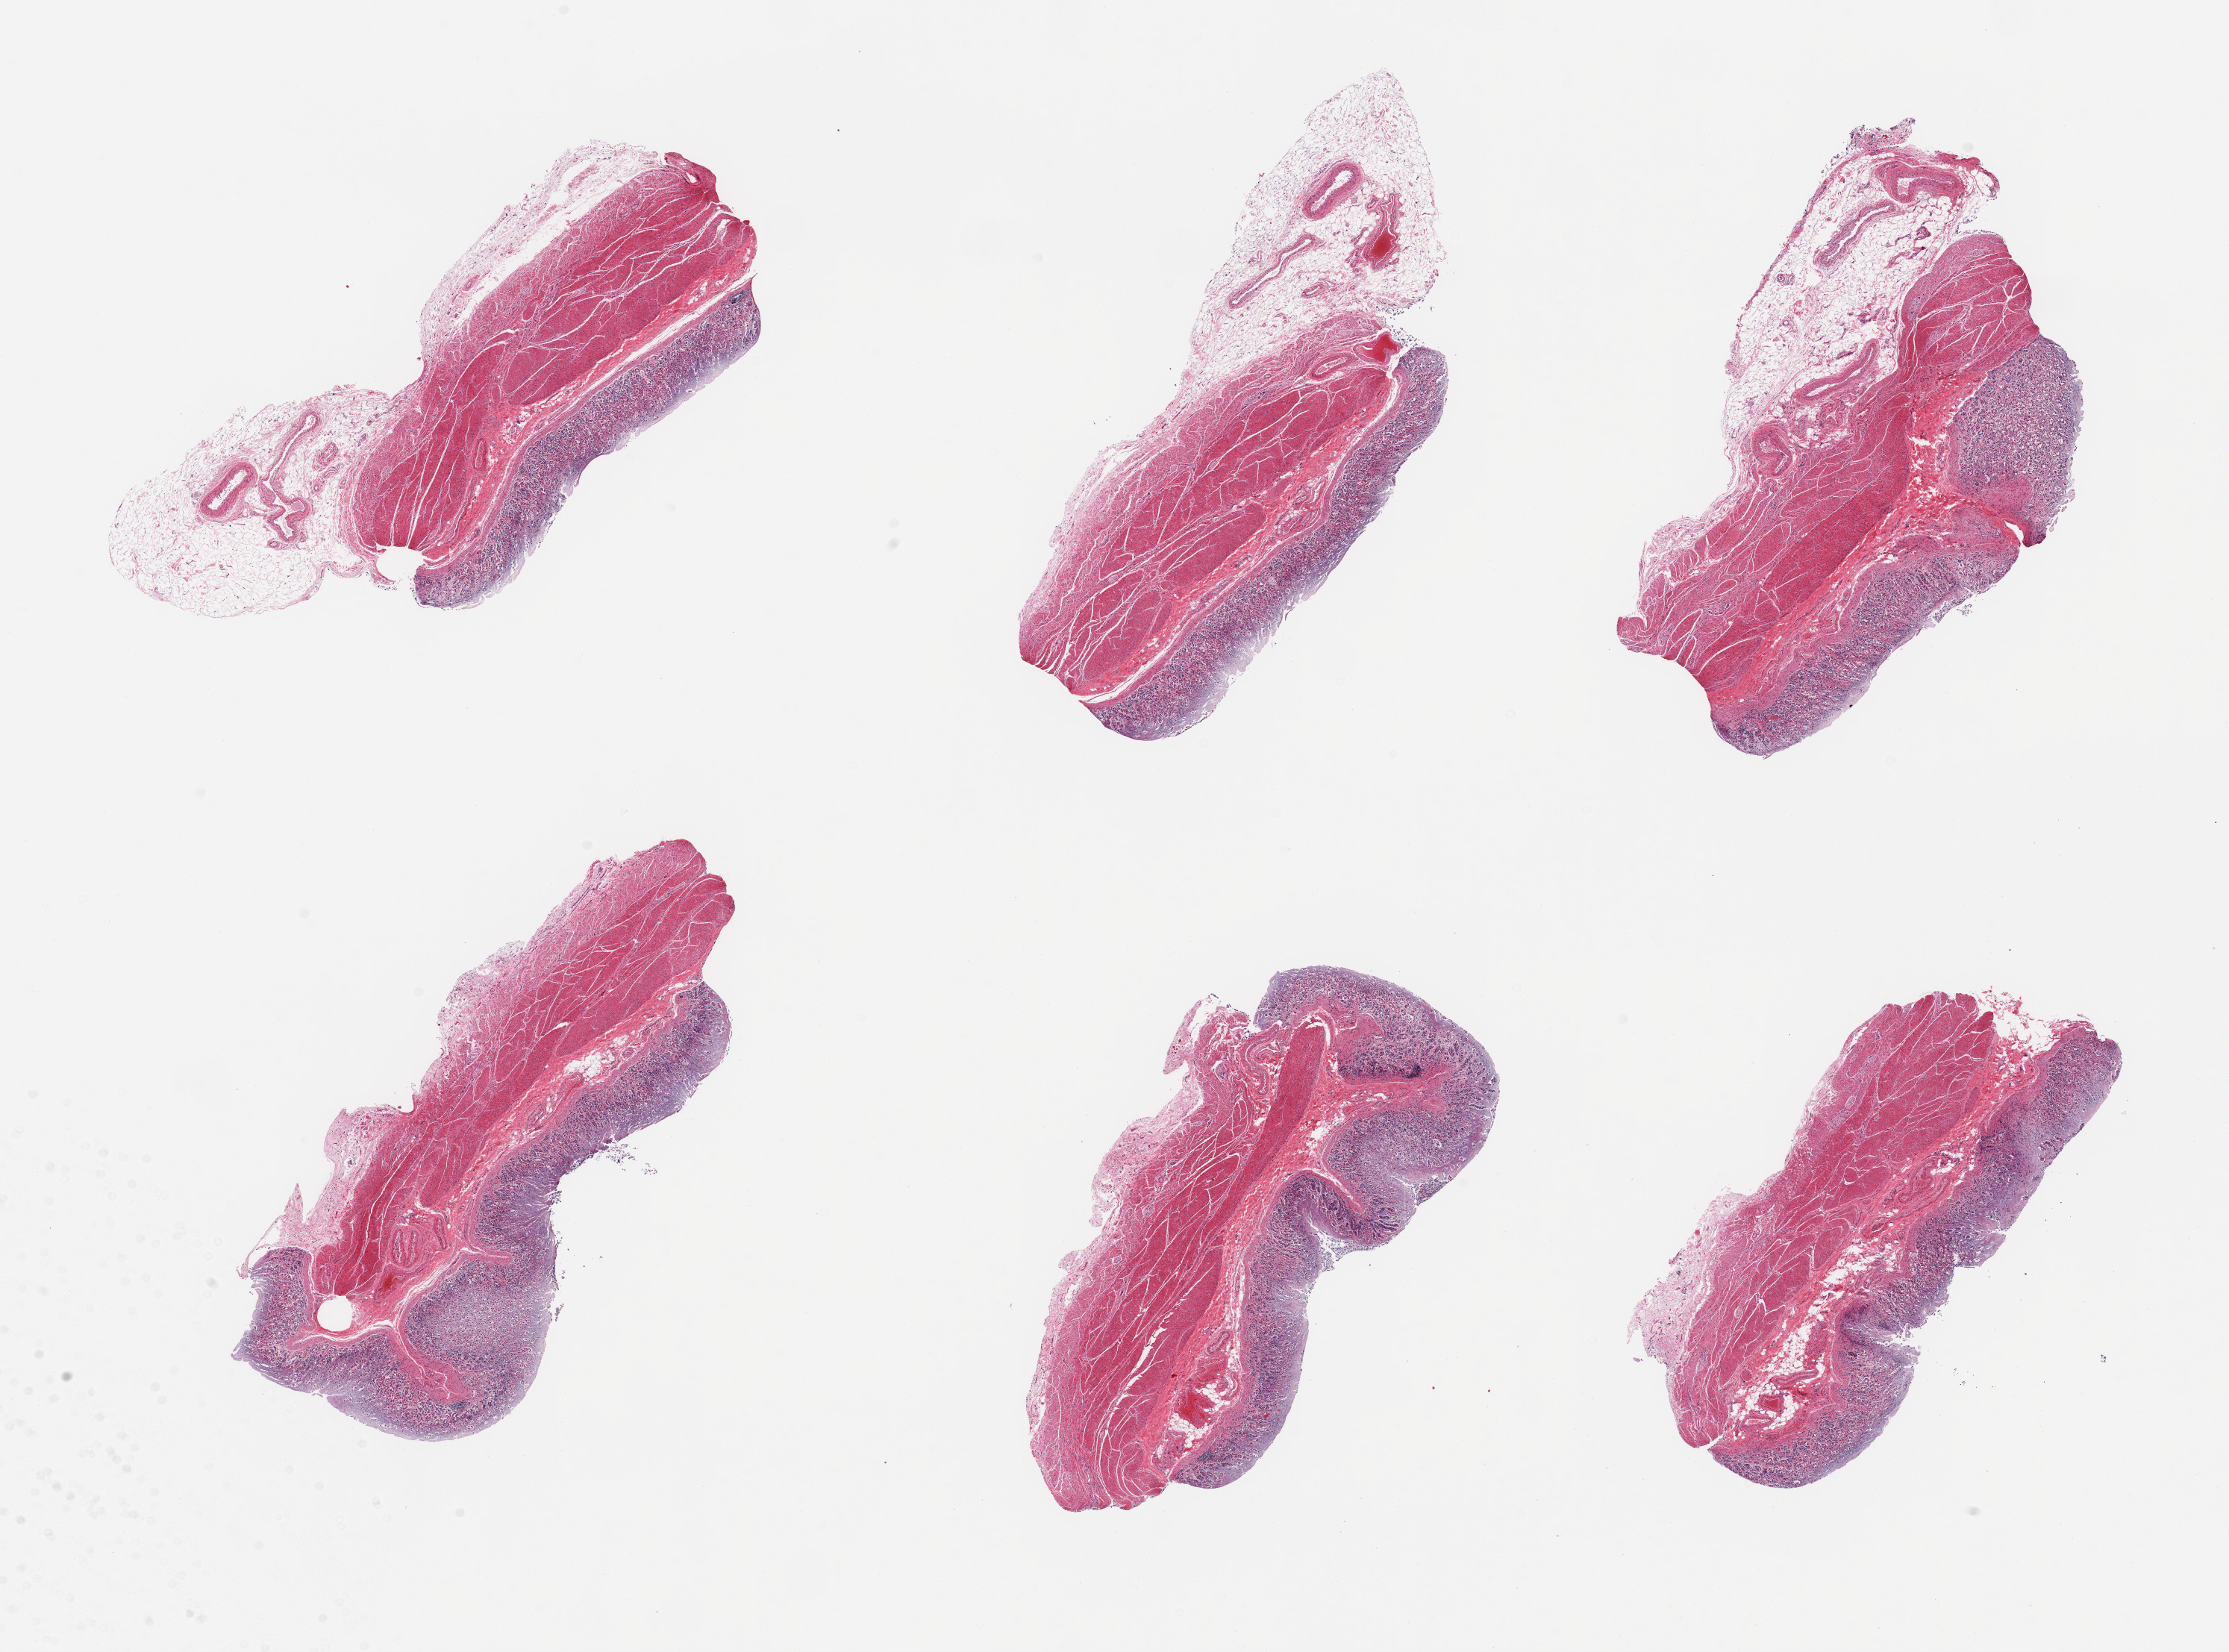
Haematoxylin and eosin whole-slide image, a low-resolution overview of the entire scanned area, about 23.6 x 17.5 mm; PAXgene-fixed paraffin-embedded (PFPE) section; target tissue: stomach; donor tissue sample. Donor: female.
Reviewer comment on this tissue sample: 6 pieces; mucosal autolysis varies from 2 to 3; muscularis intact.